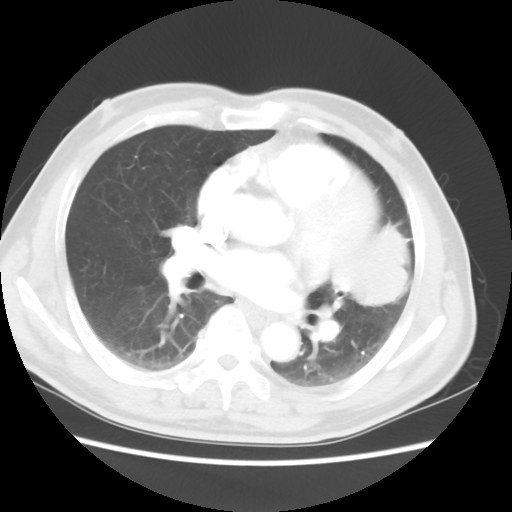
Chest CT, one axial slice; slice 24 of 50 in the series (ordered by position); reconstruction kernel STANDARD; 120 kVp; lung window (W 1500 / L -600 HU); 512 × 512 image matrix. Male patient, age 69 years. From the clinical record (not read from this slice): clinical TNM (as recorded): T3 N1 M1a.
Outlined on this slice (bounding box drawn by a radiologist):
- lung tumour (recorded histology: squamous cell carcinoma): bounding box [x1, y1, x2, y2] px = [333, 208, 420, 317]